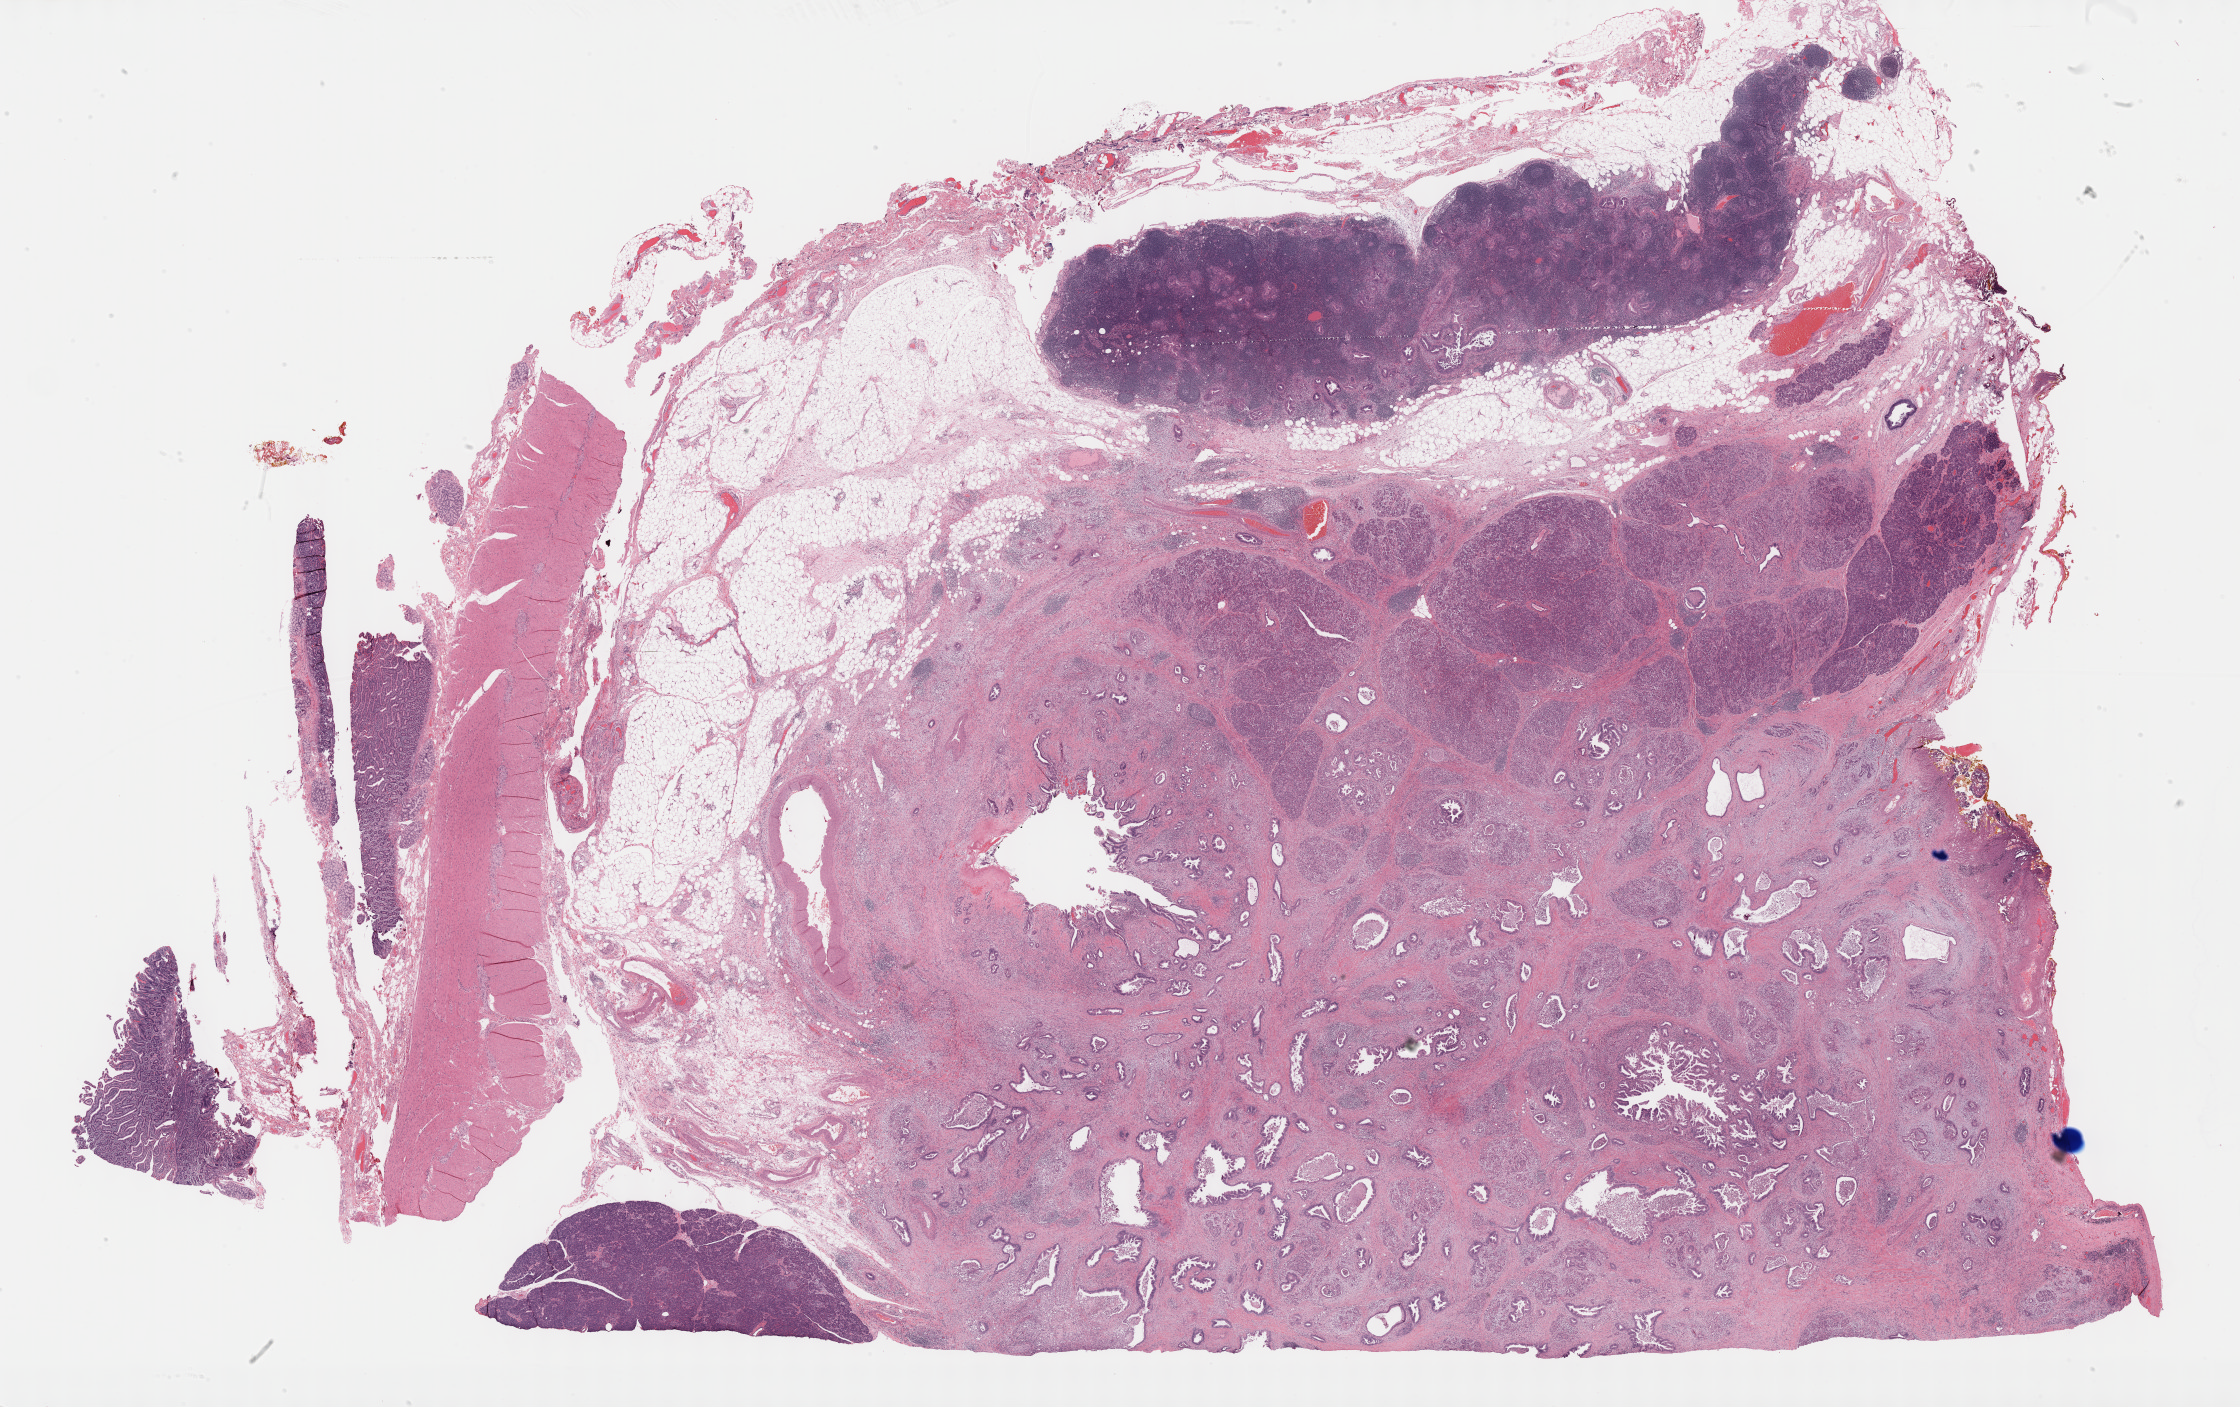
Digitized H&E tissue section (whole slide) — whole scanned area (about 36.2 x 22.8 mm, slide scanned at 40x) shown as a low-resolution overview, FFPE section, sample: primary tumour, pancreas. Patient: female, age at initial diagnosis 49 years. Histologic grade: G1 (well differentiated).
• AJCC pathologic stage: IIB (7th edition)
• lymph nodes positive (case pathology): 7 of 11 examined
• pathologic diagnosis: Infiltrating duct carcinoma, NOS